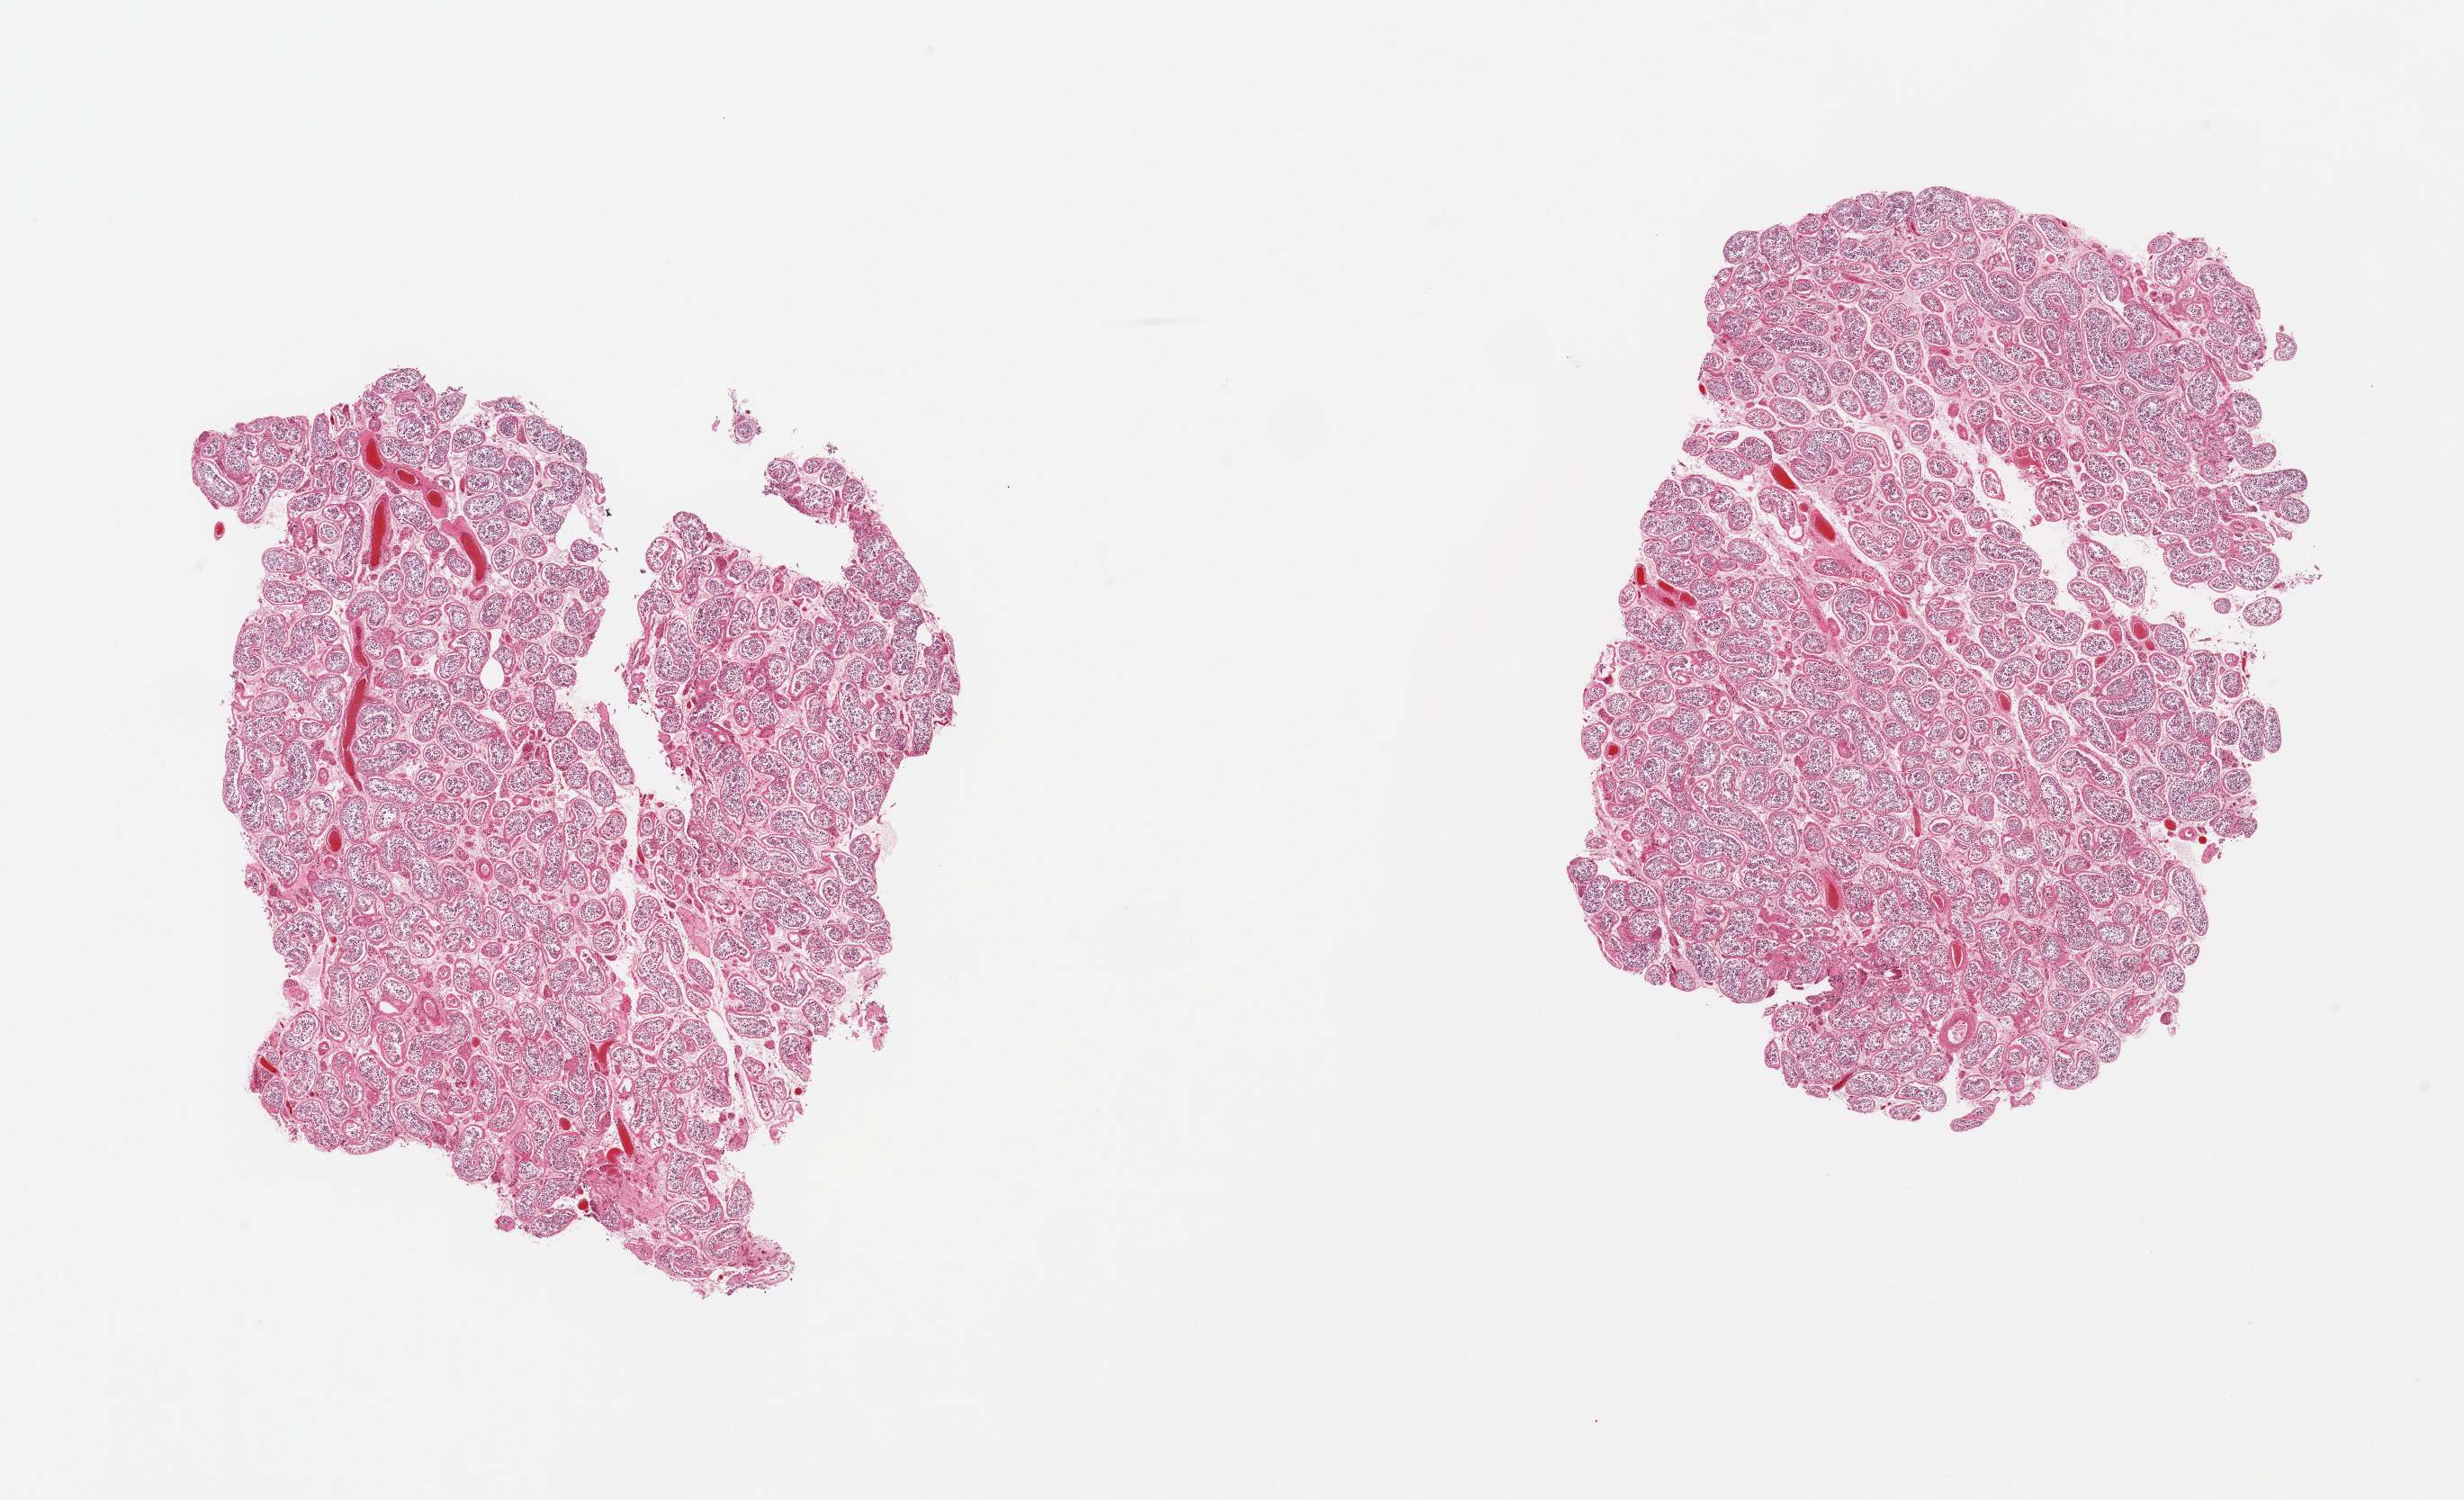
Digitized haematoxylin and eosin-stained section, brightfield — whole scanned area (about 21.7 x 13.2 mm, from a 20x scan) shown as a low-resolution overview; PAXgene-fixed paraffin-embedded (PFPE) section; section of testis (target tissue); donor tissue sample.
- pathologist's review note for this sample: 2 pieces; reduced spermatogenesis